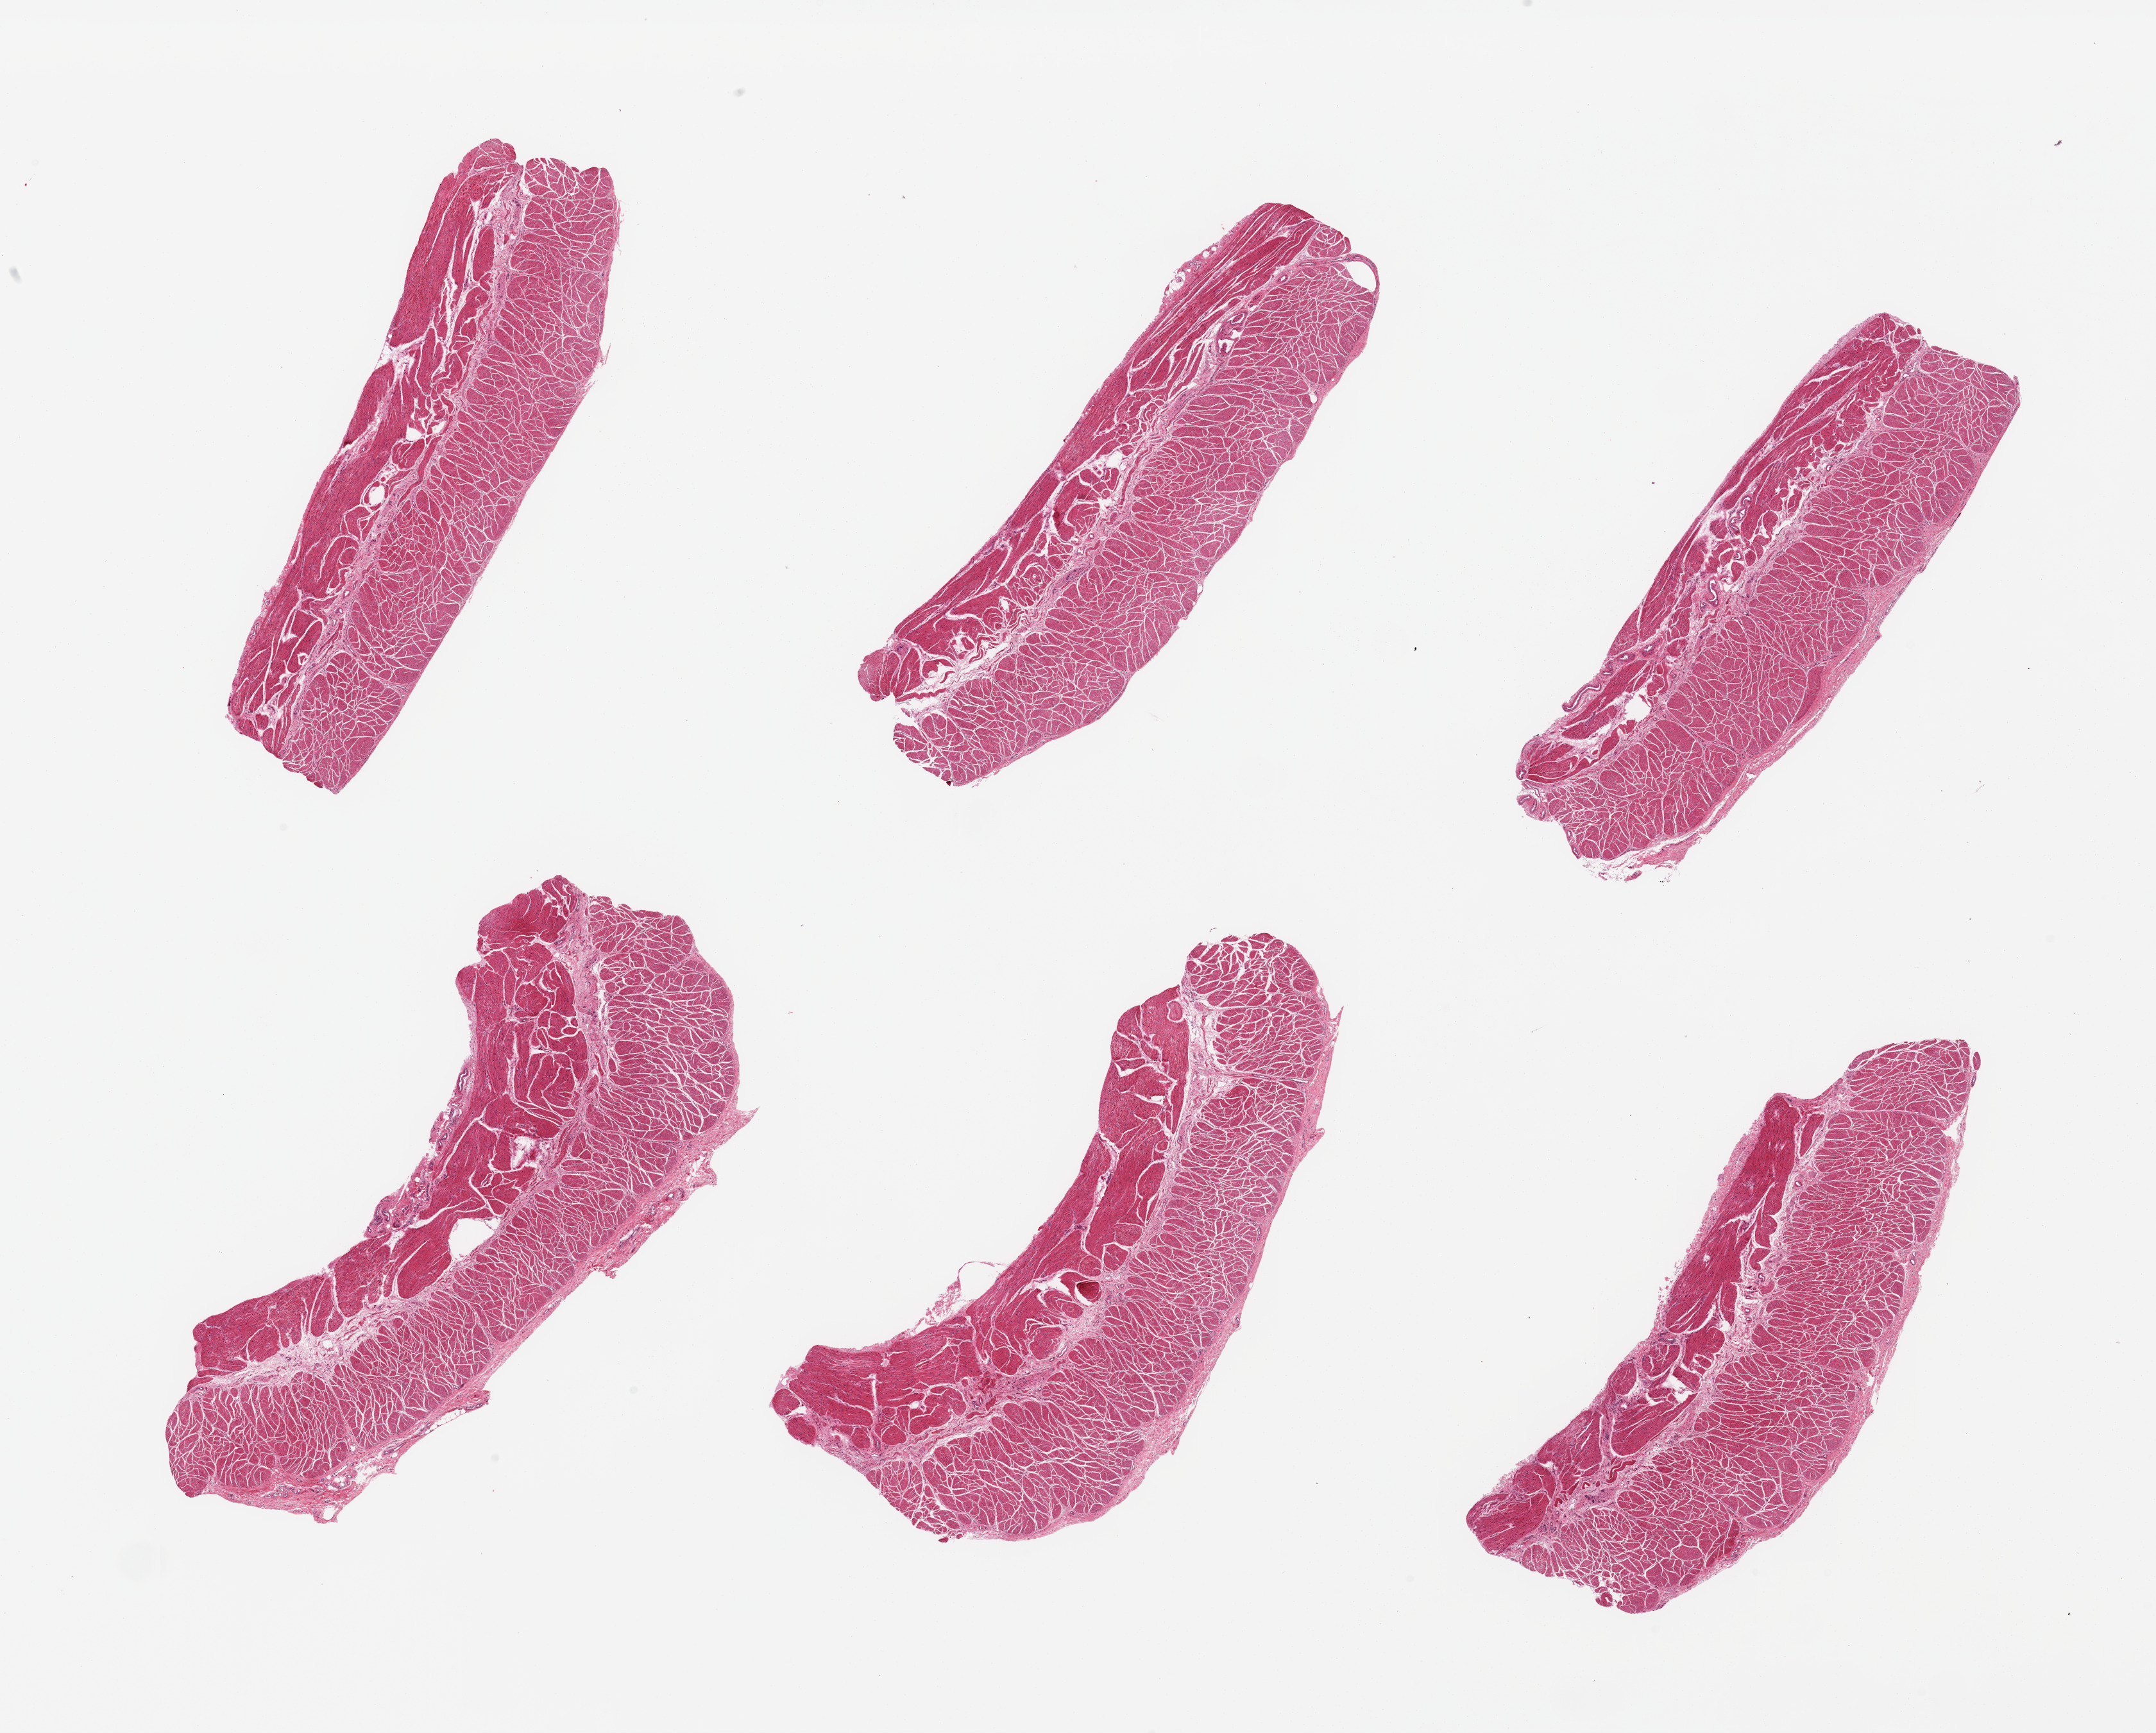
Whole-slide image, hematoxylin and eosin (H&E) stain, whole scanned area (about 26.6 x 21.4 mm, from a 20x scan) shown as a low-resolution overview, PAXgene-fixed, paraffin-embedded tissue, section of esophageal muscle (target tissue), tissue donor sample. Donor sex: male.
Pathologist's review note for this sample: 6 pieces, confirmed target muscularis.